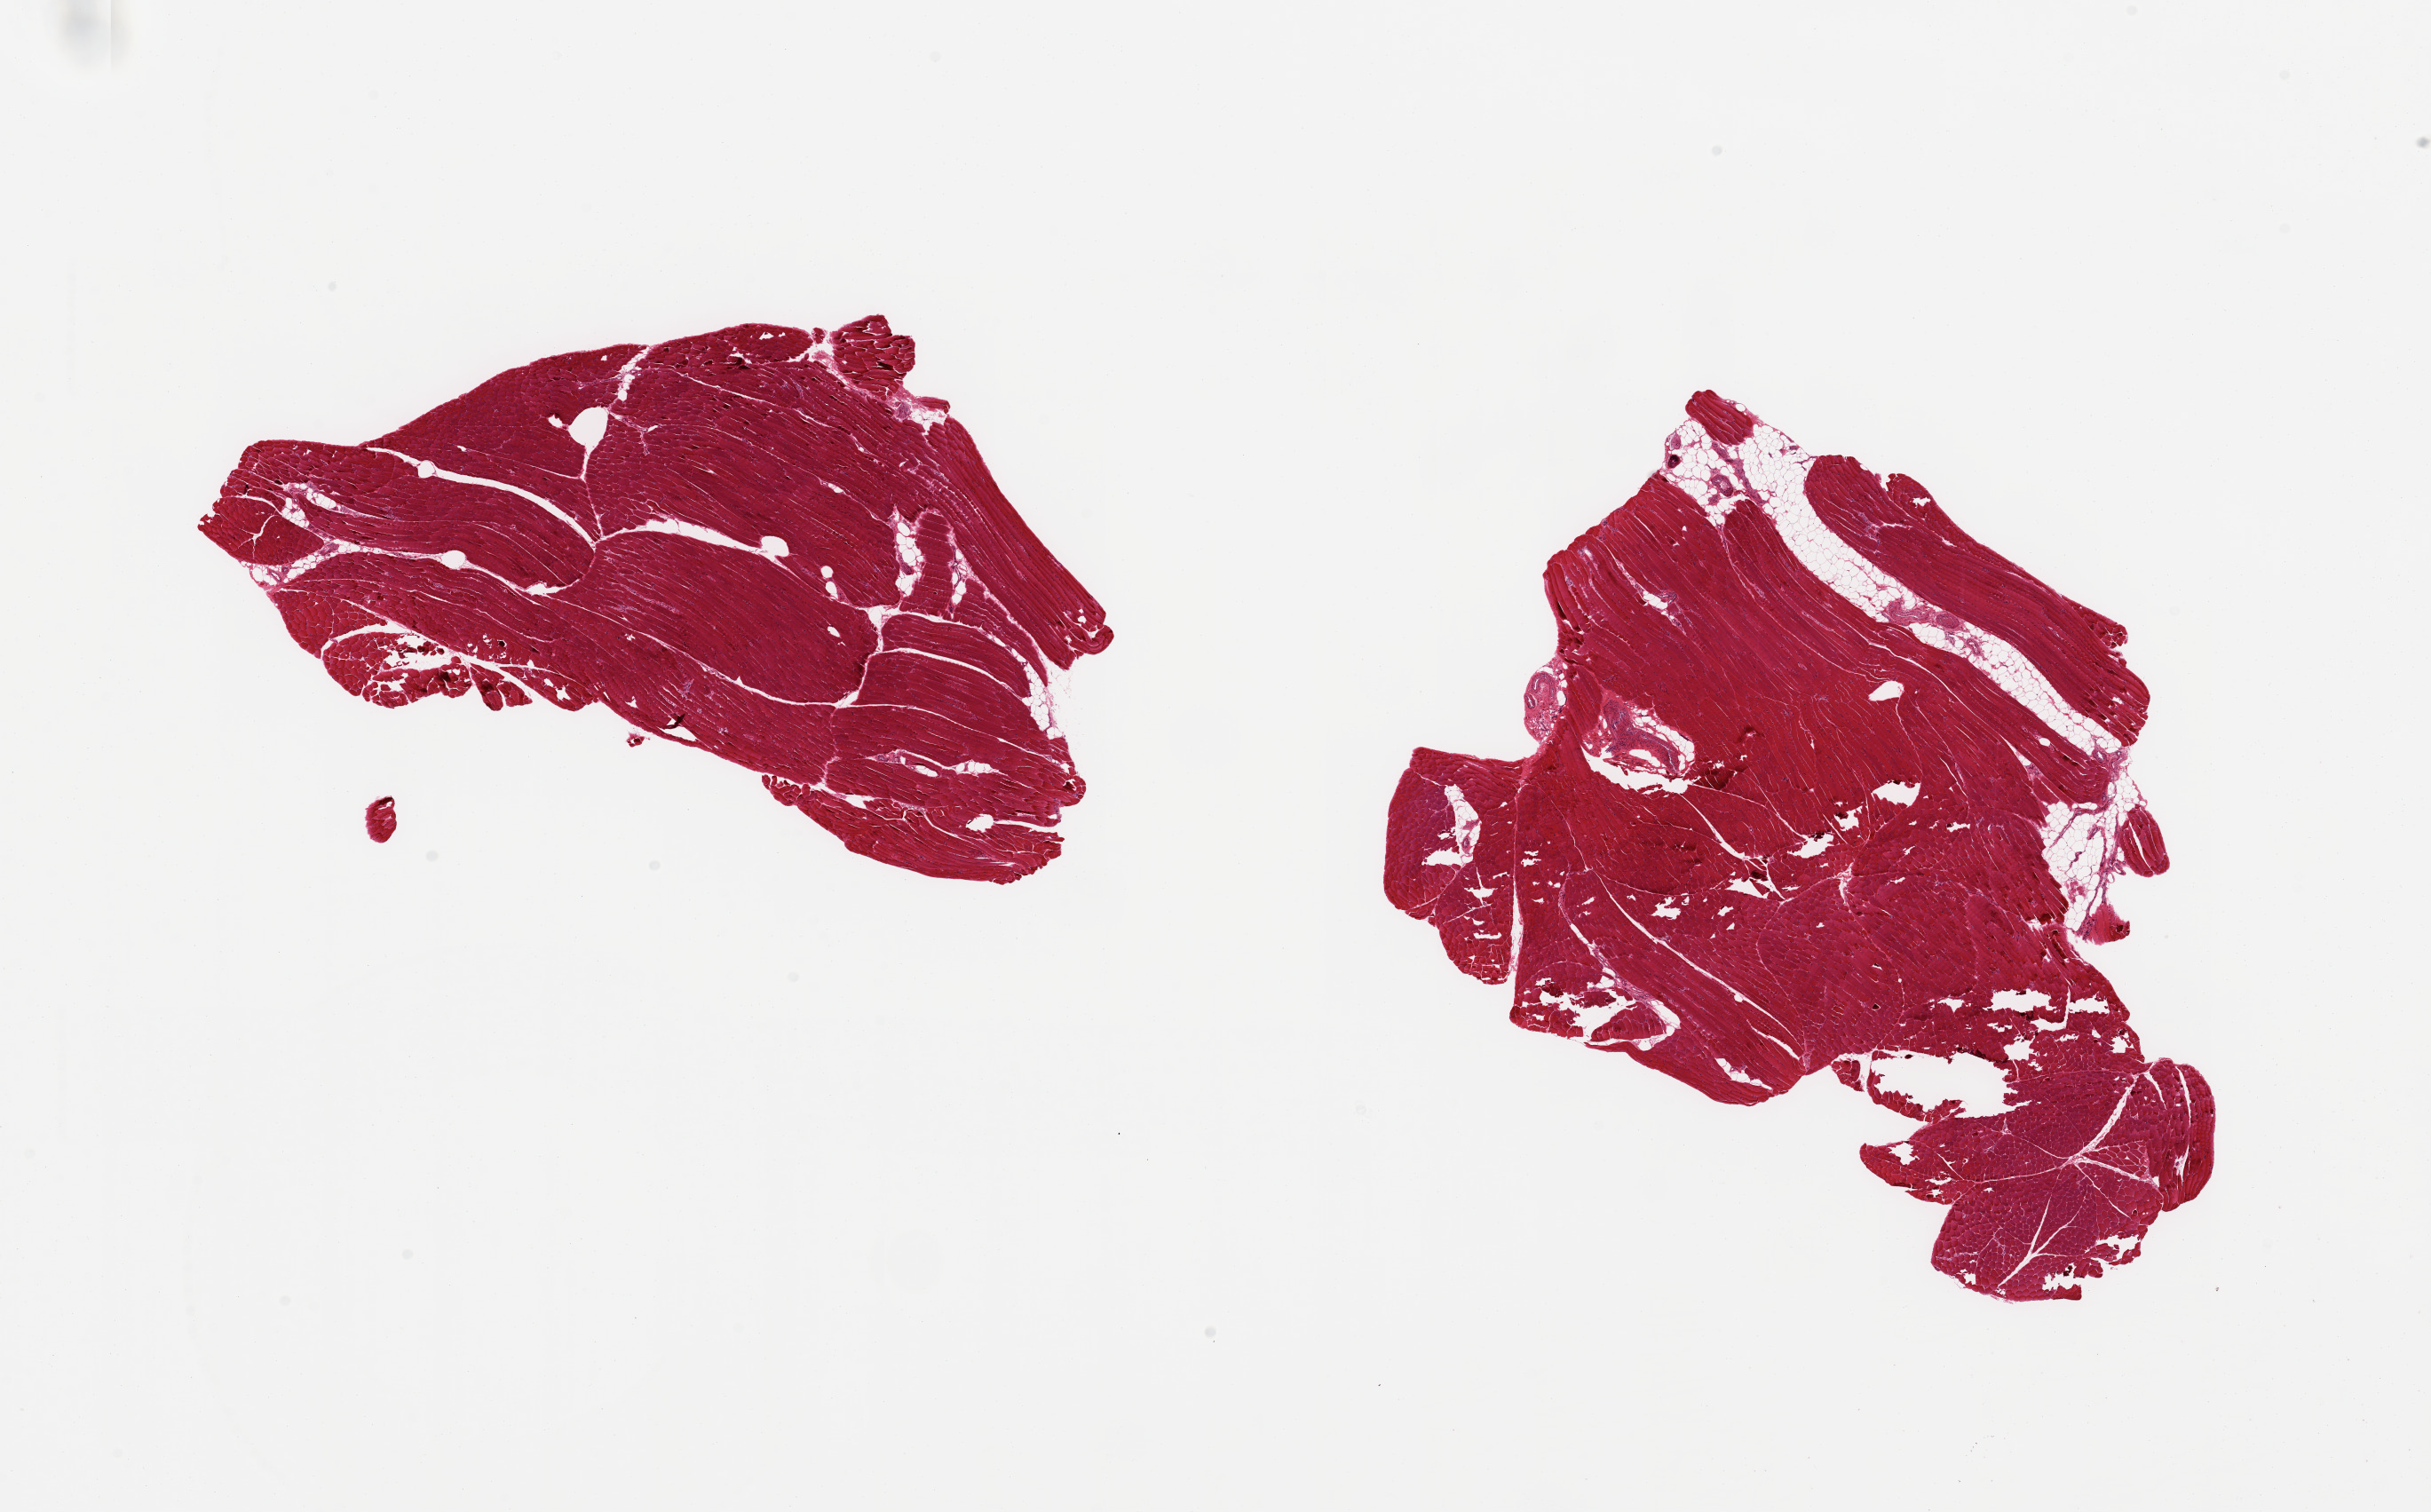
Digitized H&E-stained section — a low-resolution overview of the entire scanned area, about 21.7 x 13.5 mm (slide scanned at 20x). PAXgene-fixed paraffin-embedded (PFPE) section. Target tissue: skeletal muscle. Tissue donor sample. Donor sex: female.
Reviewer comment on this tissue sample: 2 ~8x4mm pieces, areas of poor fixation with tears/holes.